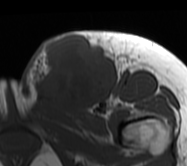
MRI of an extremity soft-tissue mass, one axial slice. Position 27 of 62 along the scan axis. MR volume resampled by the dataset authors to the PET/CT grid (not the native acquisition matrix). 3.27 mm slice thickness. 187 × 166 image matrix, field of view 183 × 162 mm. Female patient. From the clinical record (not read from this slice): histological type: leiomyosarcoma; grade: high; site of the primary tumour: groin.
Outlined on this slice (expert contour drawn on MRI and transferred to this co-registered scan by the dataset authors):
- gross tumour volume including surrounding oedema: bounding box [x1, y1, x2, y2] px = [23, 30, 133, 114]
- gross tumour volume (mass): [32, 35, 115, 111]